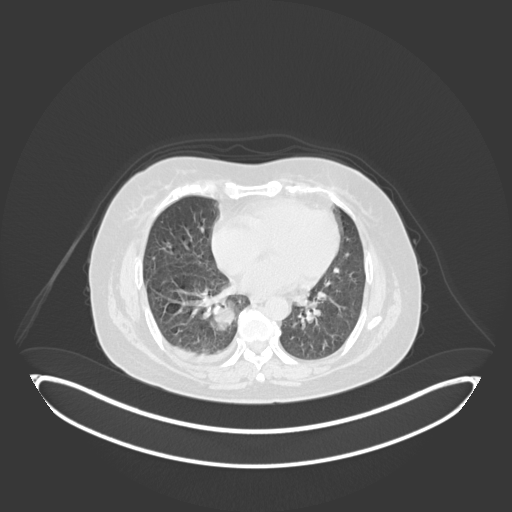
Chest CT, one axial slice; slice 62 of 231 in the series (ordered by position); 120 kVp; lung window (W 1500 / L -600 HU); 1 mm slice thickness; 512 × 512 image matrix. Patient: female, 56 years. From the clinical record (not read from this slice): clinical TNM (as recorded): T2b N1 M0.
Outlined on this slice (bounding box drawn by a radiologist):
- lung tumour (recorded histology: small cell carcinoma): bounding box (x1, y1, x2, y2) in pixels: (212, 301, 243, 337)